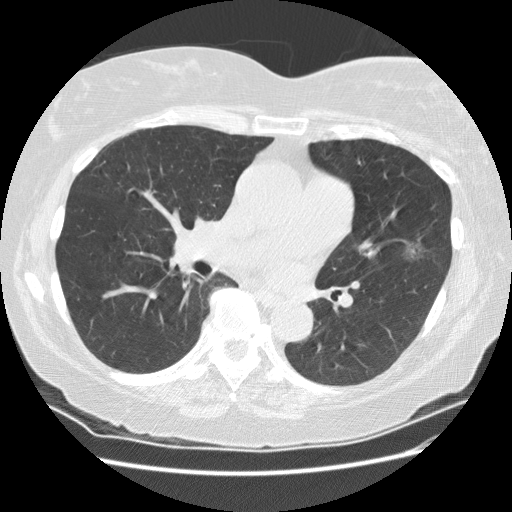
Low-dose screening chest CT, one axial slice. Slice 96 of 180 in the series (ordered by position). Reconstruction kernel STANDARD. 120 kVp. Lung window (W 1500 / L -600 HU). 512 × 512 image matrix, field of view 360 × 360 mm.
Structures marked on this image (outlined manually by an expert reader):
- lesion 1 (tumor, upper lobe of left lung): bounding box <406,242,430,260> (left, top, right, bottom; pixels)